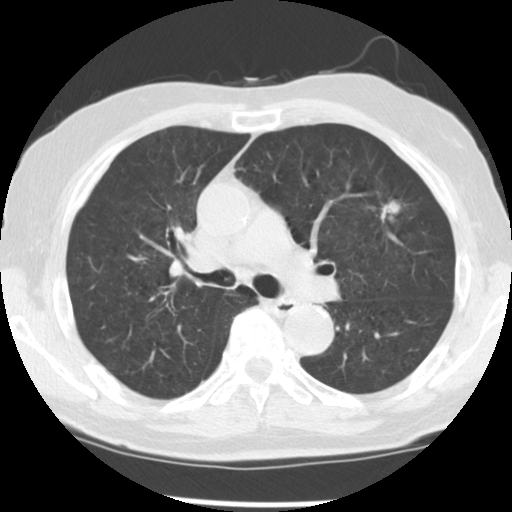
Chest CT (low-dose screening protocol), one axial image. Third annual screen. Lung window (W 1500 / L -600 HU). Standard (soft-tissue) reconstruction kernel (STANDARD). 140 kVp. Male, age 70 years at enrolment. Current smoker at enrolment.
Lesion marked by an expert reader, box from (x=356, y=184) to (x=414, y=243) px. The screening reader recorded 3 non-calcified nodules or masses ≥4 mm on this exam; which of them this box marks is not recorded. Official screen result: positive, other. Participant outcome: lung cancer diagnosed 74 days after this screen — adenocarcinoma, NOS, left upper lobe, moderately differentiated (G2), stage IIIA (AJCC 6th edition), 17 mm at pathology.